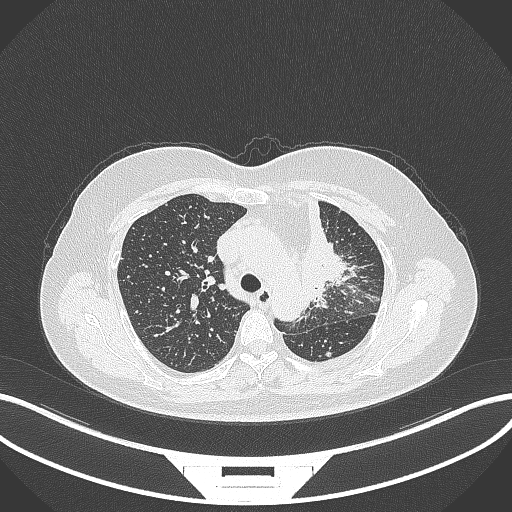
Chest CT, one axial slice; slice 239 of 348 in the series (ordered by position); lung window (W 1500 / L -600 HU); 1 mm slice thickness; 512 × 512 image matrix, field of view 400 × 400 mm. Patient: female, 49 years. Case-level facts recorded for this patient, not image findings: clinical TNM (as recorded): T1c N0 M1.
Outlined on this slice (bounding box drawn by a radiologist):
- lung tumour (recorded histology: adenocarcinoma): bounding box <295,197,355,302> (left, top, right, bottom; pixels)